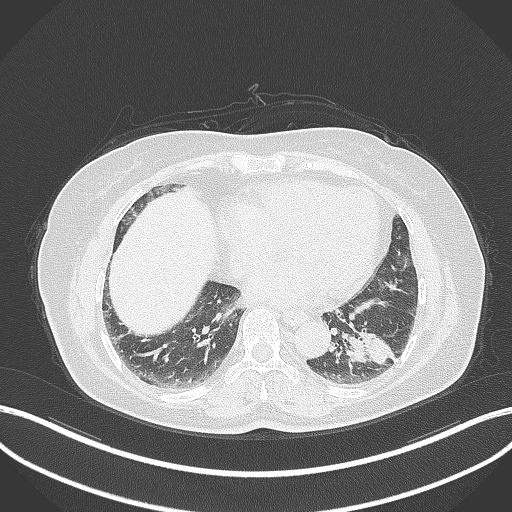
Chest CT, one axial slice. Slice 136 of 311 in the series (ordered by position). Lung window (W 1500 / L -600 HU). 1 mm slice thickness. 512 × 512 image matrix. Patient: female, 59 years. From the clinical record (not read from this slice): clinical TNM (as recorded): T2a N0 M0; histopathological grade: G2-3.
Outlined on this slice (rectangle marked by the reading radiologist):
- lung tumour (recorded histology: adenocarcinoma): bounding box [x1, y1, x2, y2] px = [341, 325, 397, 373]